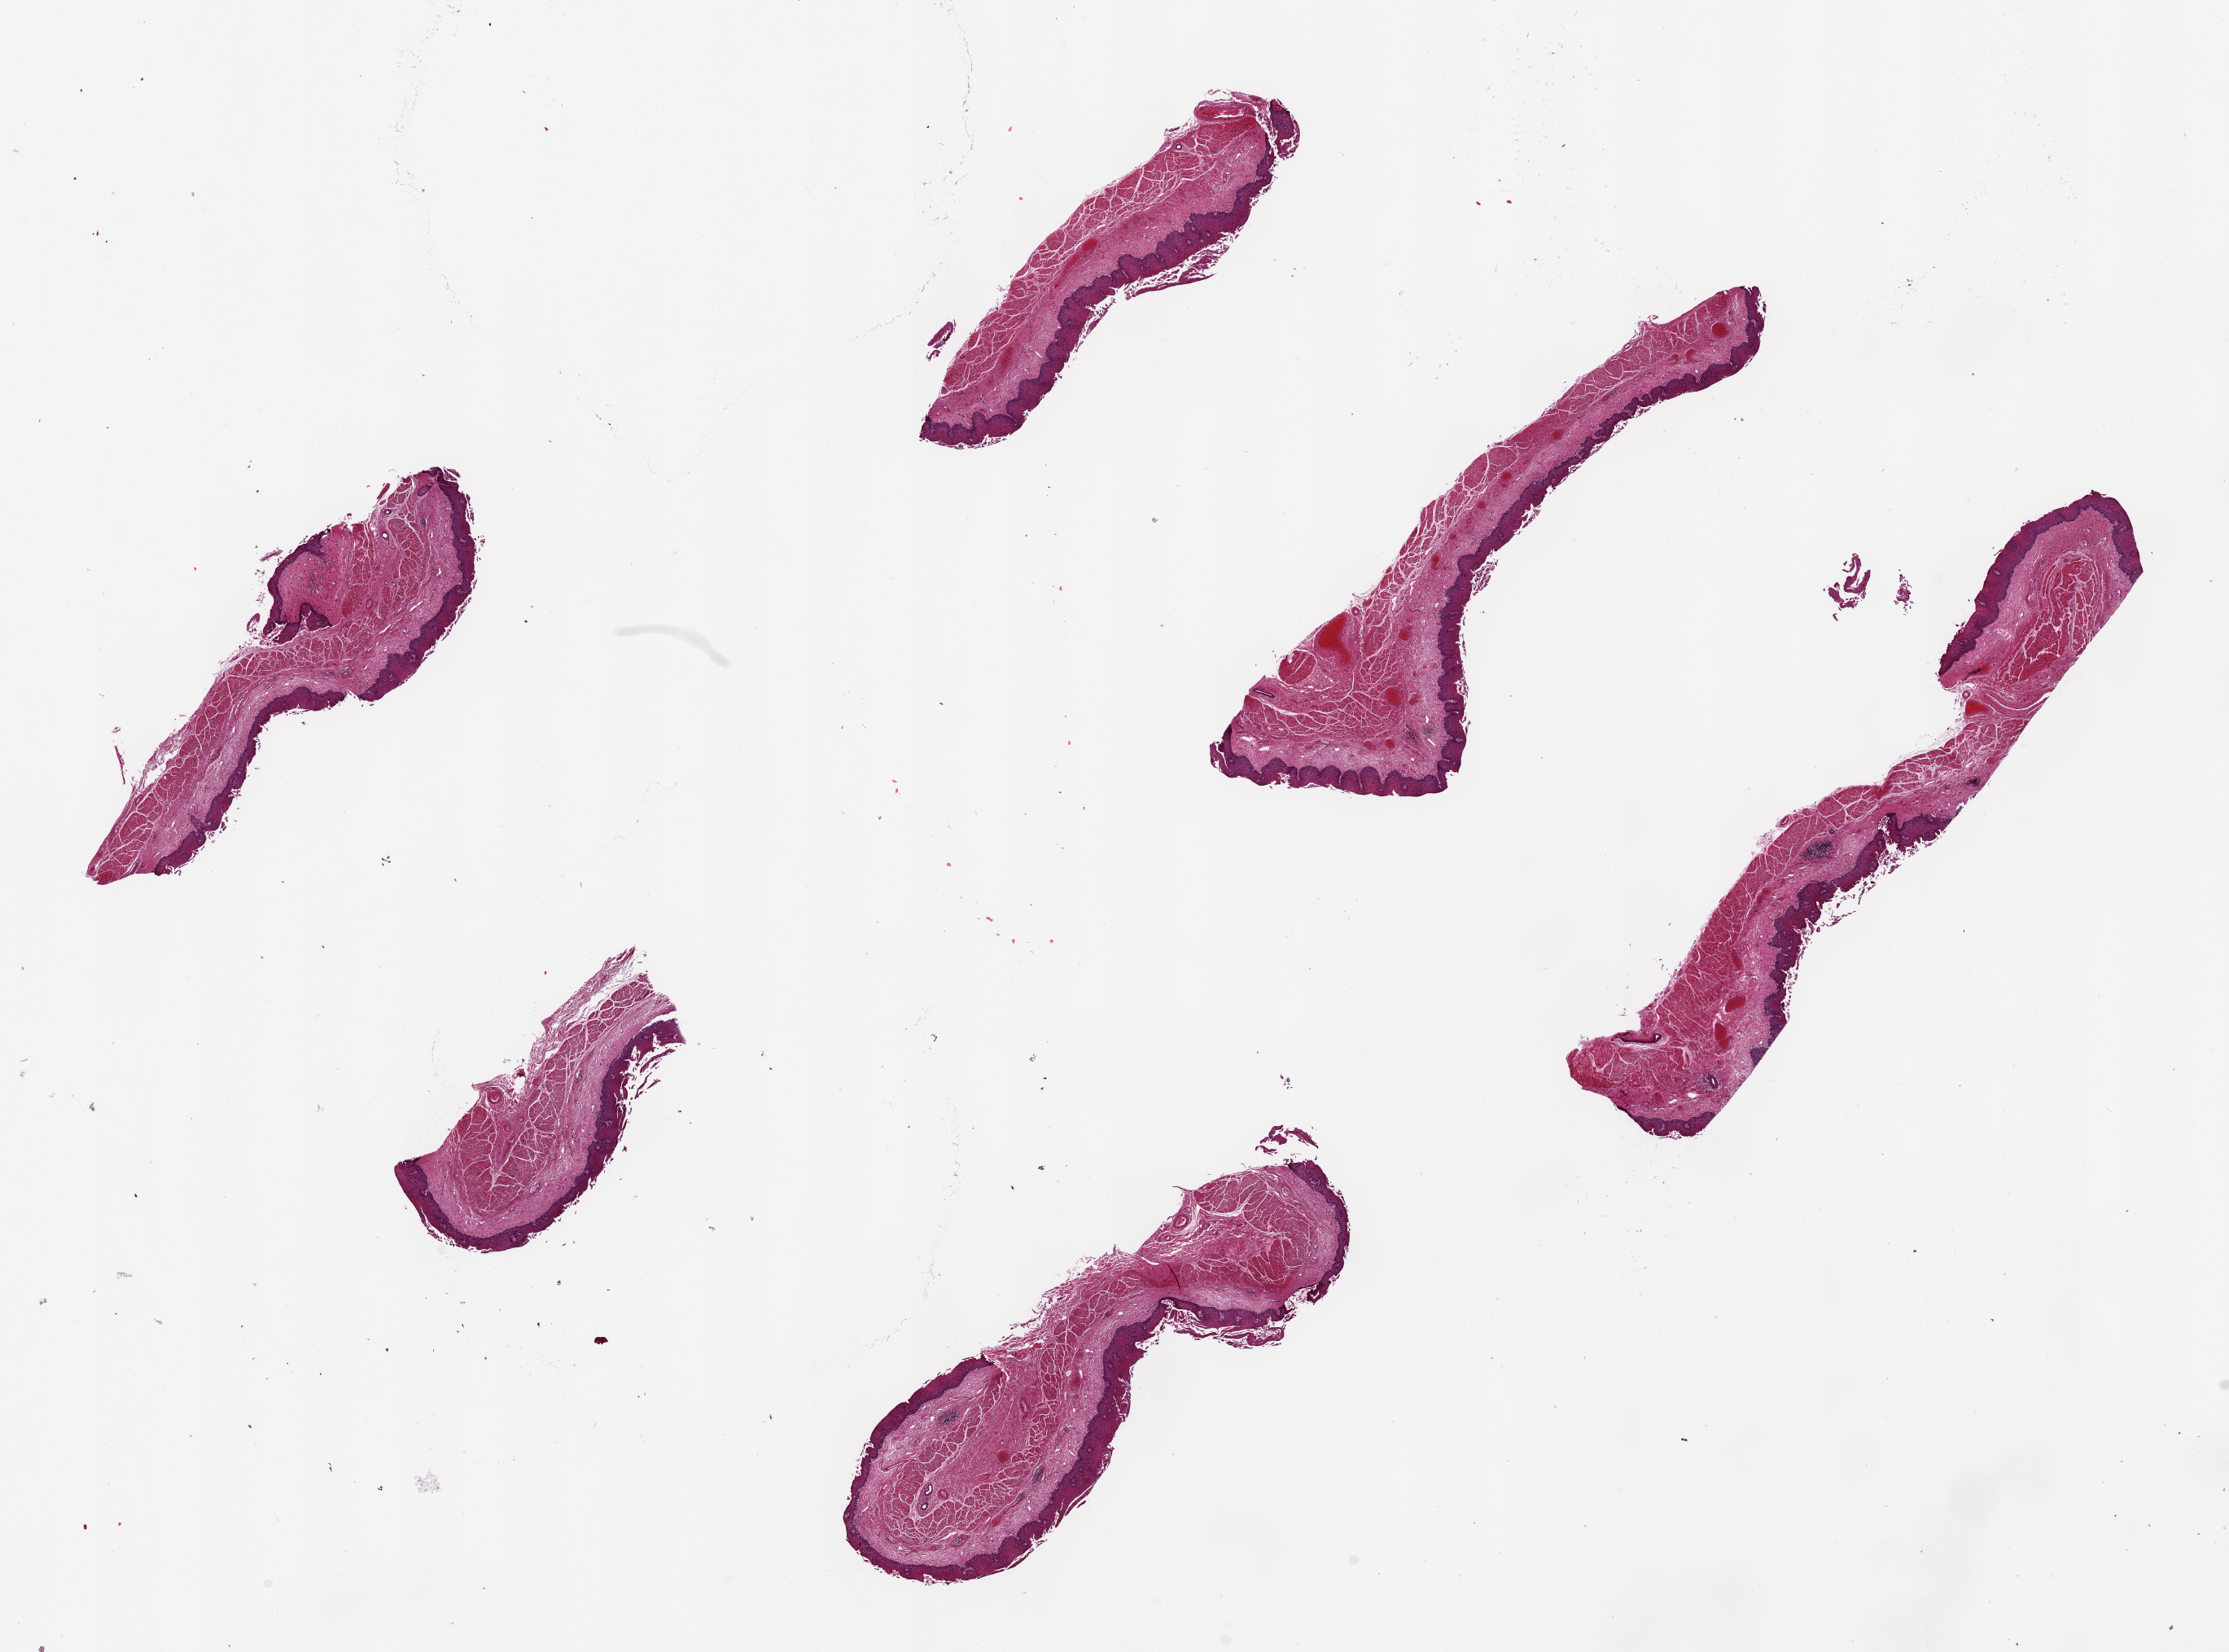
Digitized hematoxylin and eosin (H&E)-stained section, whole scanned area (about 21.7 x 16.0 mm, from a 20x scan) shown as a low-resolution overview, PAXgene-fixed, paraffin-embedded tissue, sampled site (target tissue): esophageal mucous membrane, tissue donor sample. Female donor.
- pathologist's review note for this sample: 6 pieces, 6.5x1.5mm. Squamous mucosa is ~10-15% of thickness